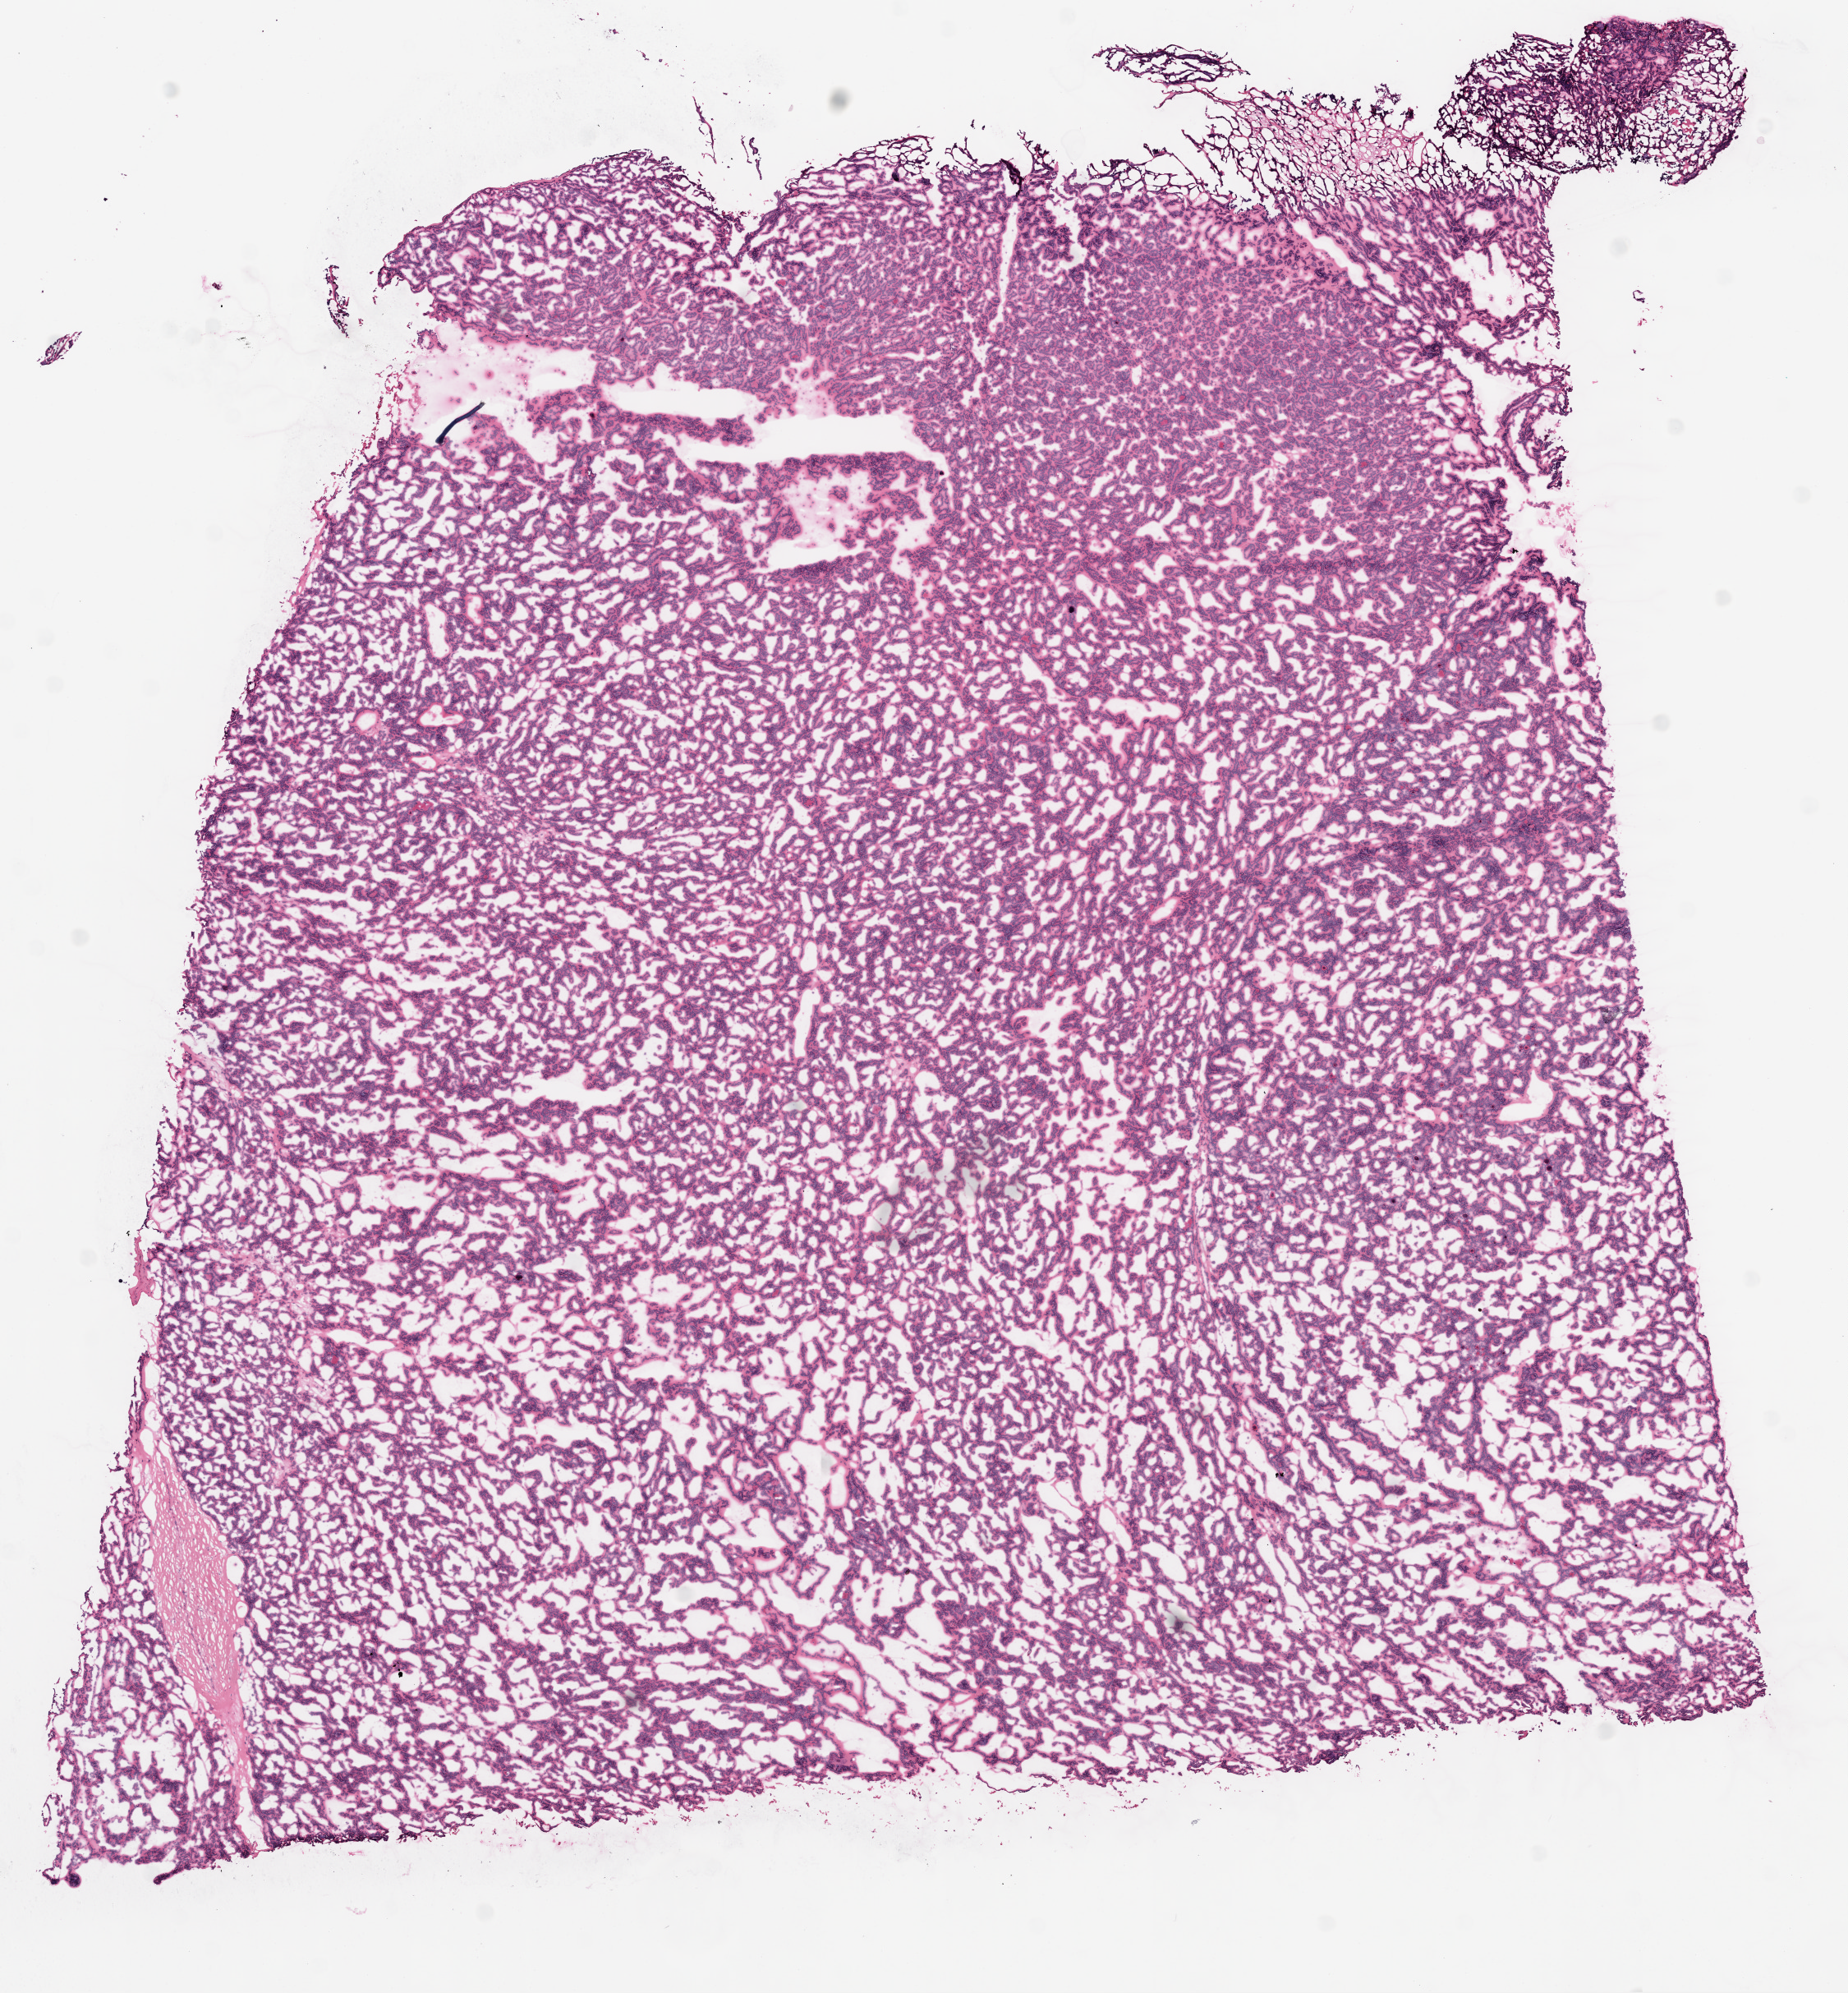
Digitized H&E tissue section (whole slide), whole scanned area (about 9.0 x 9.7 mm, slide scanned at 20x) shown as a low-resolution overview; frozen section from the top of the tissue portion; primary tumour sample from the kidney. Female, age 54 years at initial diagnosis. Slide review estimates, as recorded: tumour cells 92%, tumour nuclei 80%, normal cells 0%, stromal cells 5%, necrosis 3%.
* laterality: left
* diagnosis: Papillary adenocarcinoma, NOS